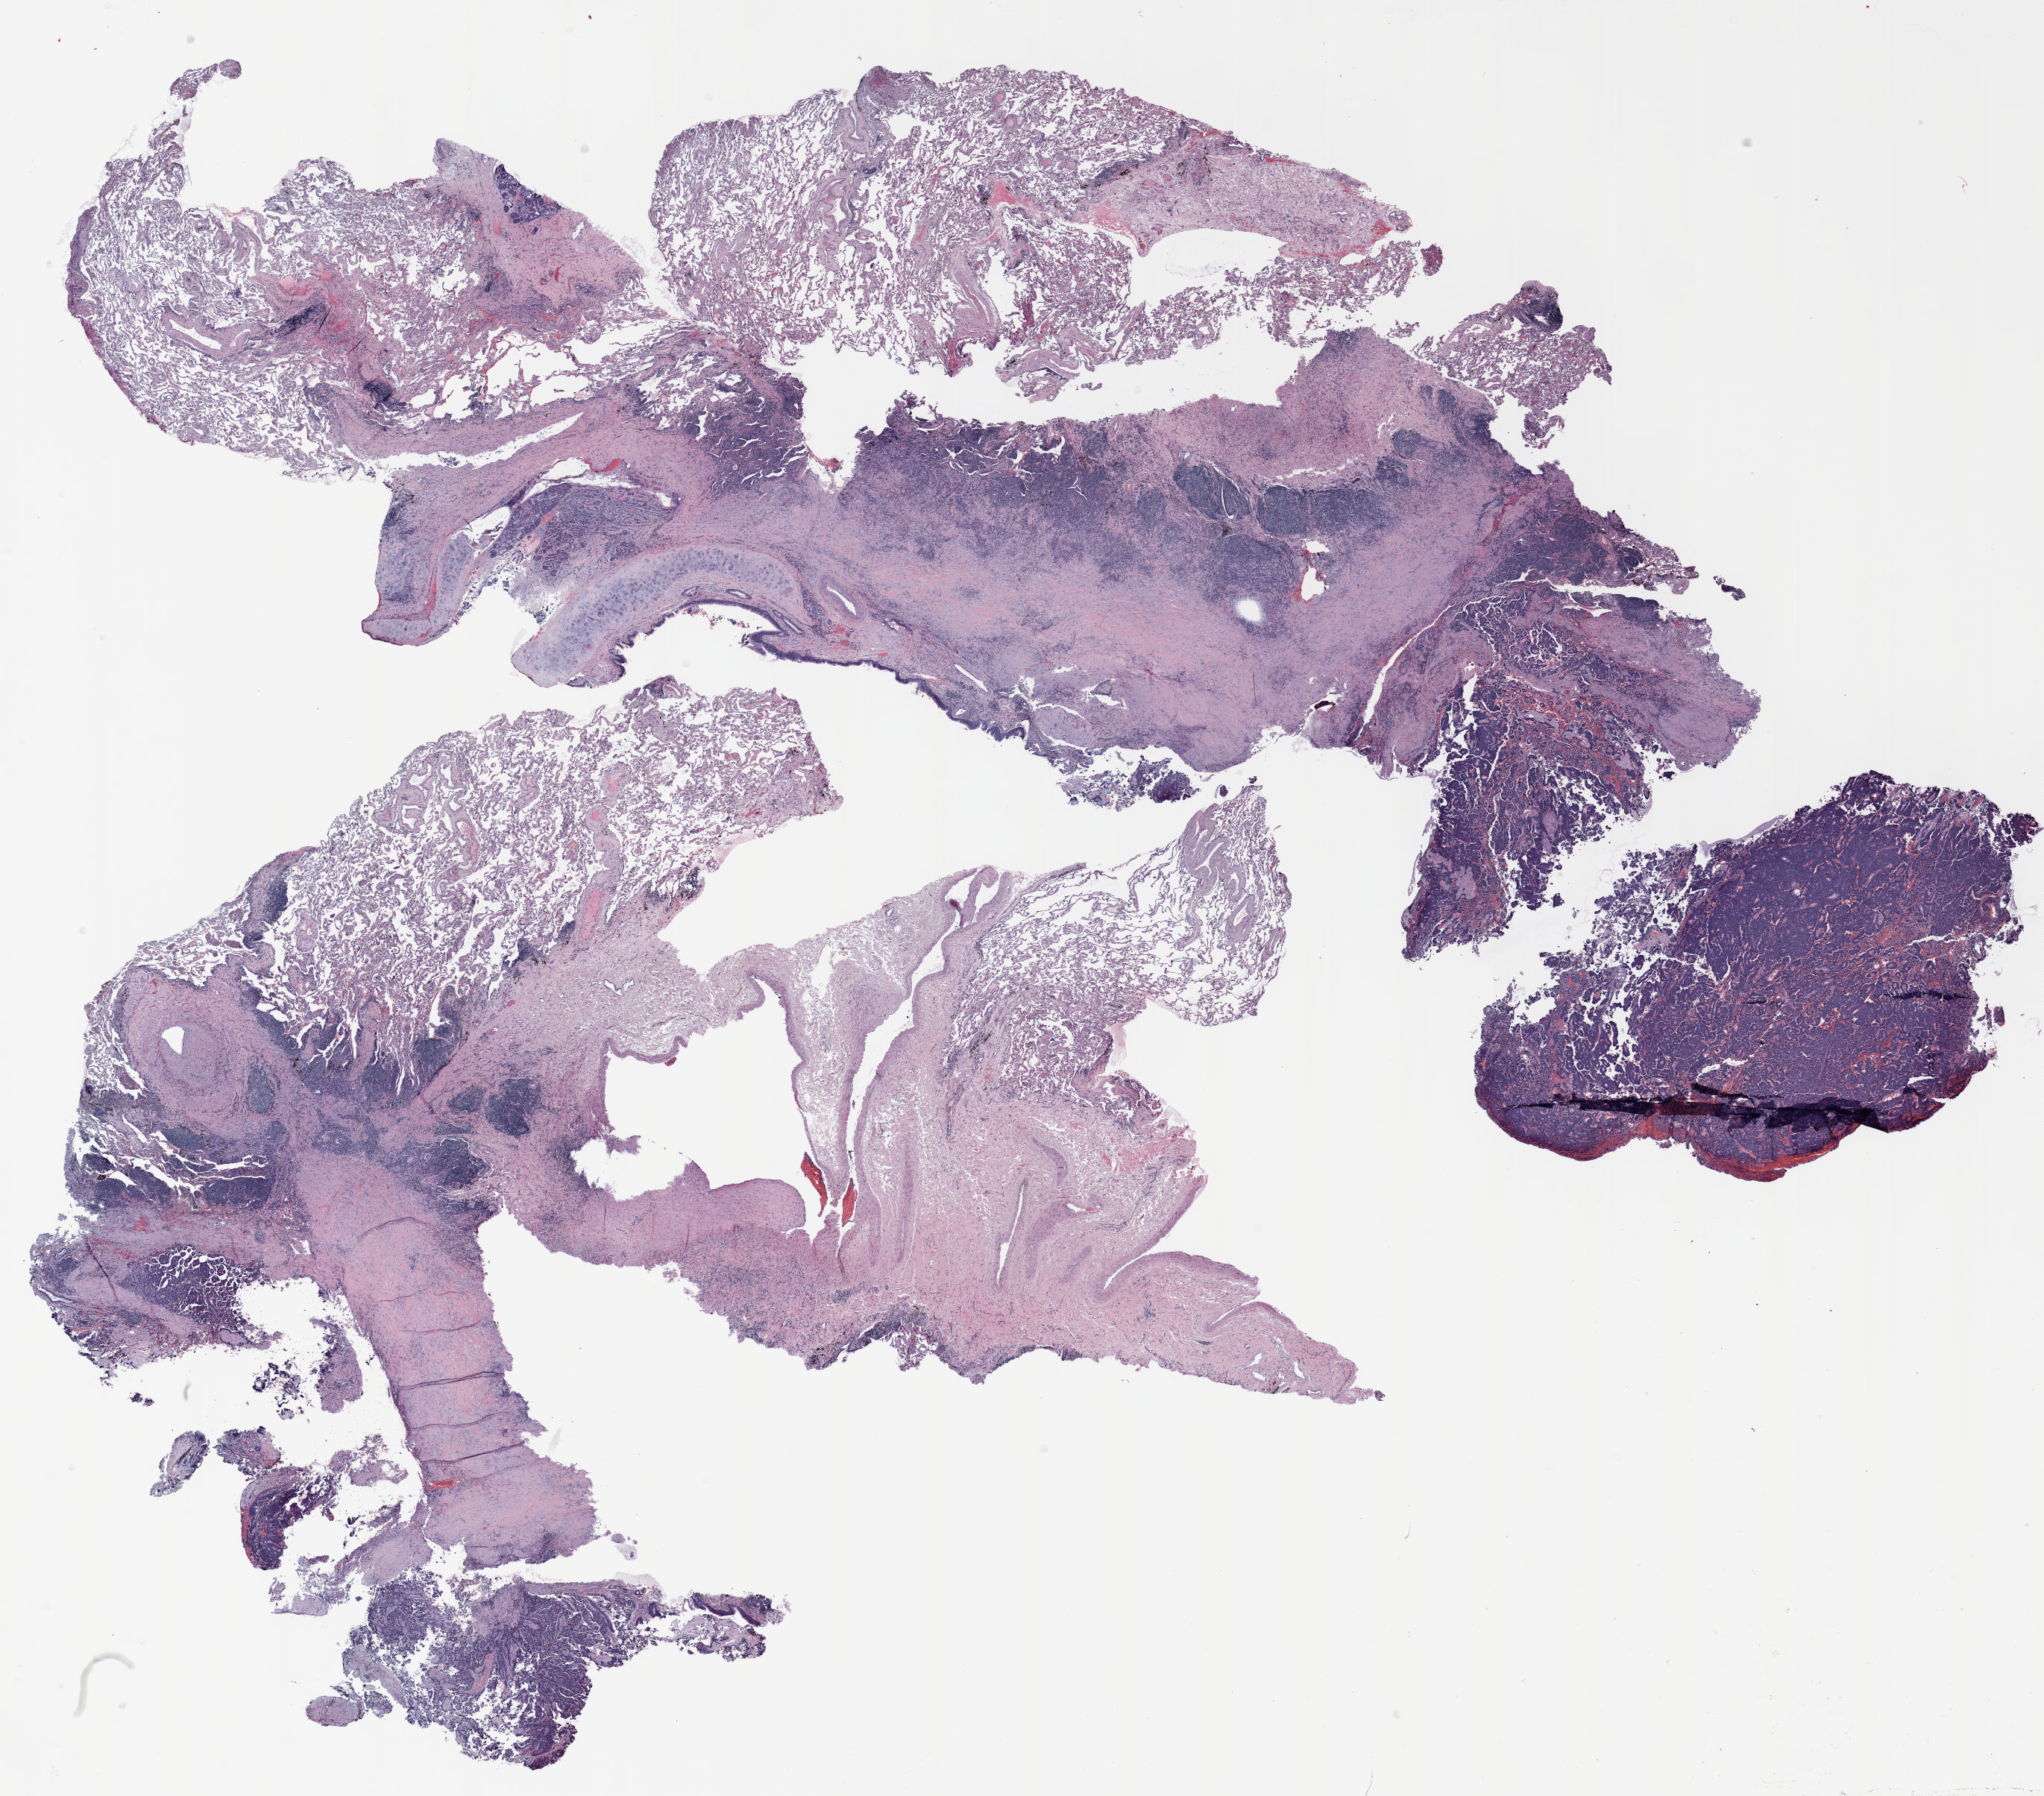
Whole-slide histology image, Hematoxylin and eosin (H&E) stained, whole scanned area (about 22.0 x 19.4 mm, slide scanned at 20x) shown as a low-resolution overview; FFPE section; lung. Male, age 73 at enrolment. Grade: cannot be assessed (GX).
Participant's lung-cancer diagnosis: Carcinoid tumor, NOS. ICD-O-3 topography: lower lobe of lung (C34.3). Tumour size (pathology): 12 mm. Stage (AJCC 6th edition): carcinoid, stage not assessed. Primary tumour location (clinical record): right lower lobe.